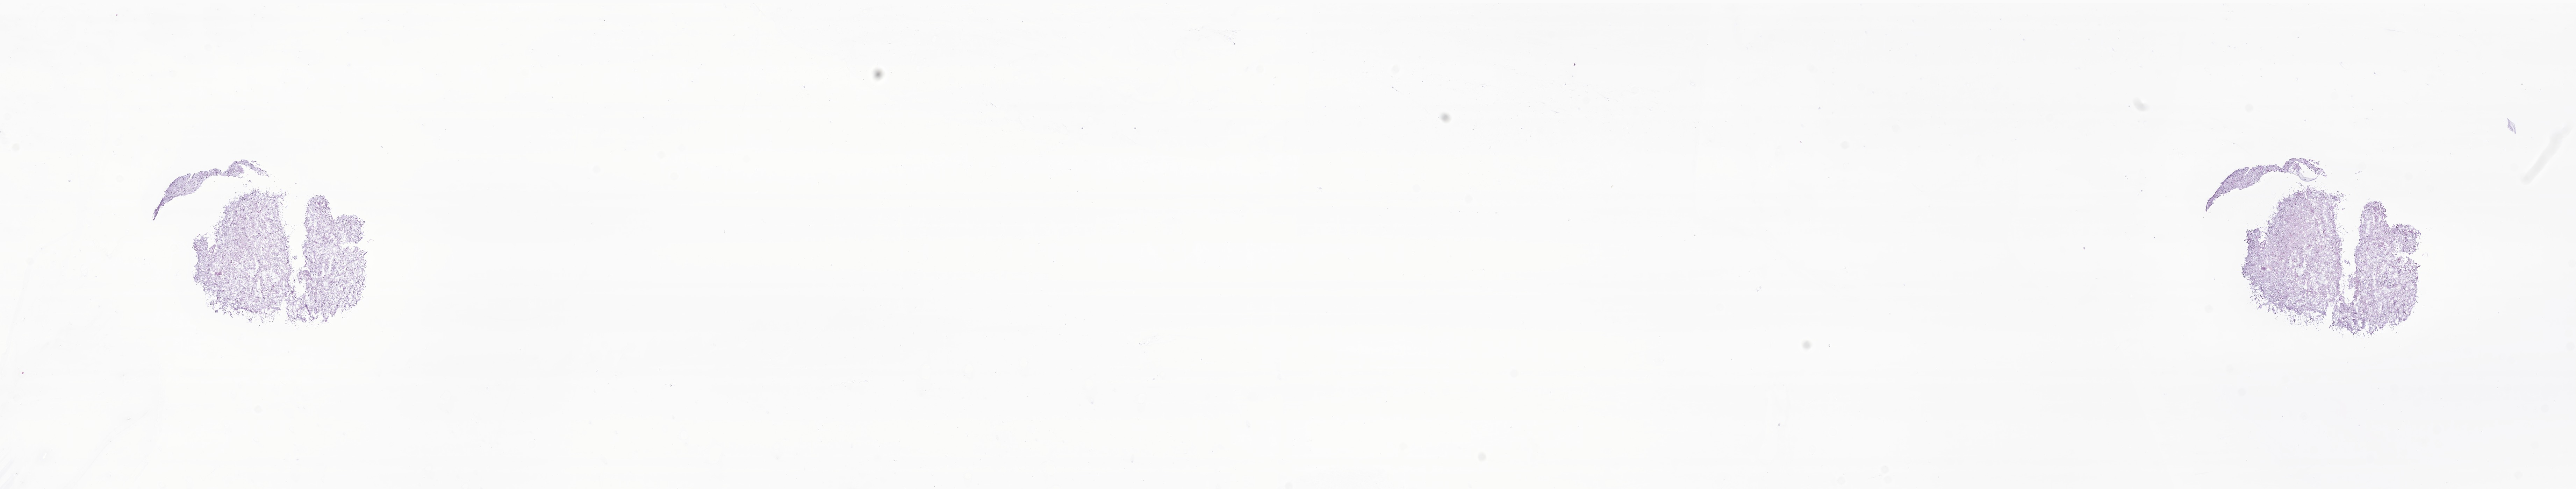
Digitized hematoxylin and eosin (H&E)-stained section of tumor tissue from the brain, a low-resolution overview of the entire scanned area, about 31.1 x 5.9 mm; cryosection (OCT / tissue freezing medium). Male patient, age 203 months (16 years 11 months).
- diagnosis: Neoplasm, uncertain whether benign or malignant